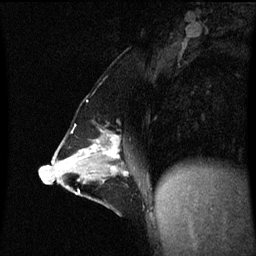
Breast MRI (dynamic contrast-enhanced), one sagittal slice; position 28 of 60 along the scan axis; dynamic contrast-enhanced series, image 2 of 3 at this slice position (ordered by acquisition); 1.5 T; TE 4.2 ms, TR 8.9 ms; 2 mm slice thickness; 256 × 256 image matrix, field of view 200 × 200 mm. Female patient, age 47 years. From the clinical record (not read from this slice): setting: breast cancer imaged before/during neoadjuvant chemotherapy; receptor status: HR-positive, HER2-negative.
Annotated regions visible in this slice (semi-automatically segmented with operator editing):
- analysis volume of interest (the breast-tissue region the enhancement analysis was run in; not a lesion): bounding box <53,130,146,209> (left, top, right, bottom; pixels)
- tumour enhancement mask (voxels above the 70 % enhancement threshold inside the analysis volume of interest): <80,136,129,175>